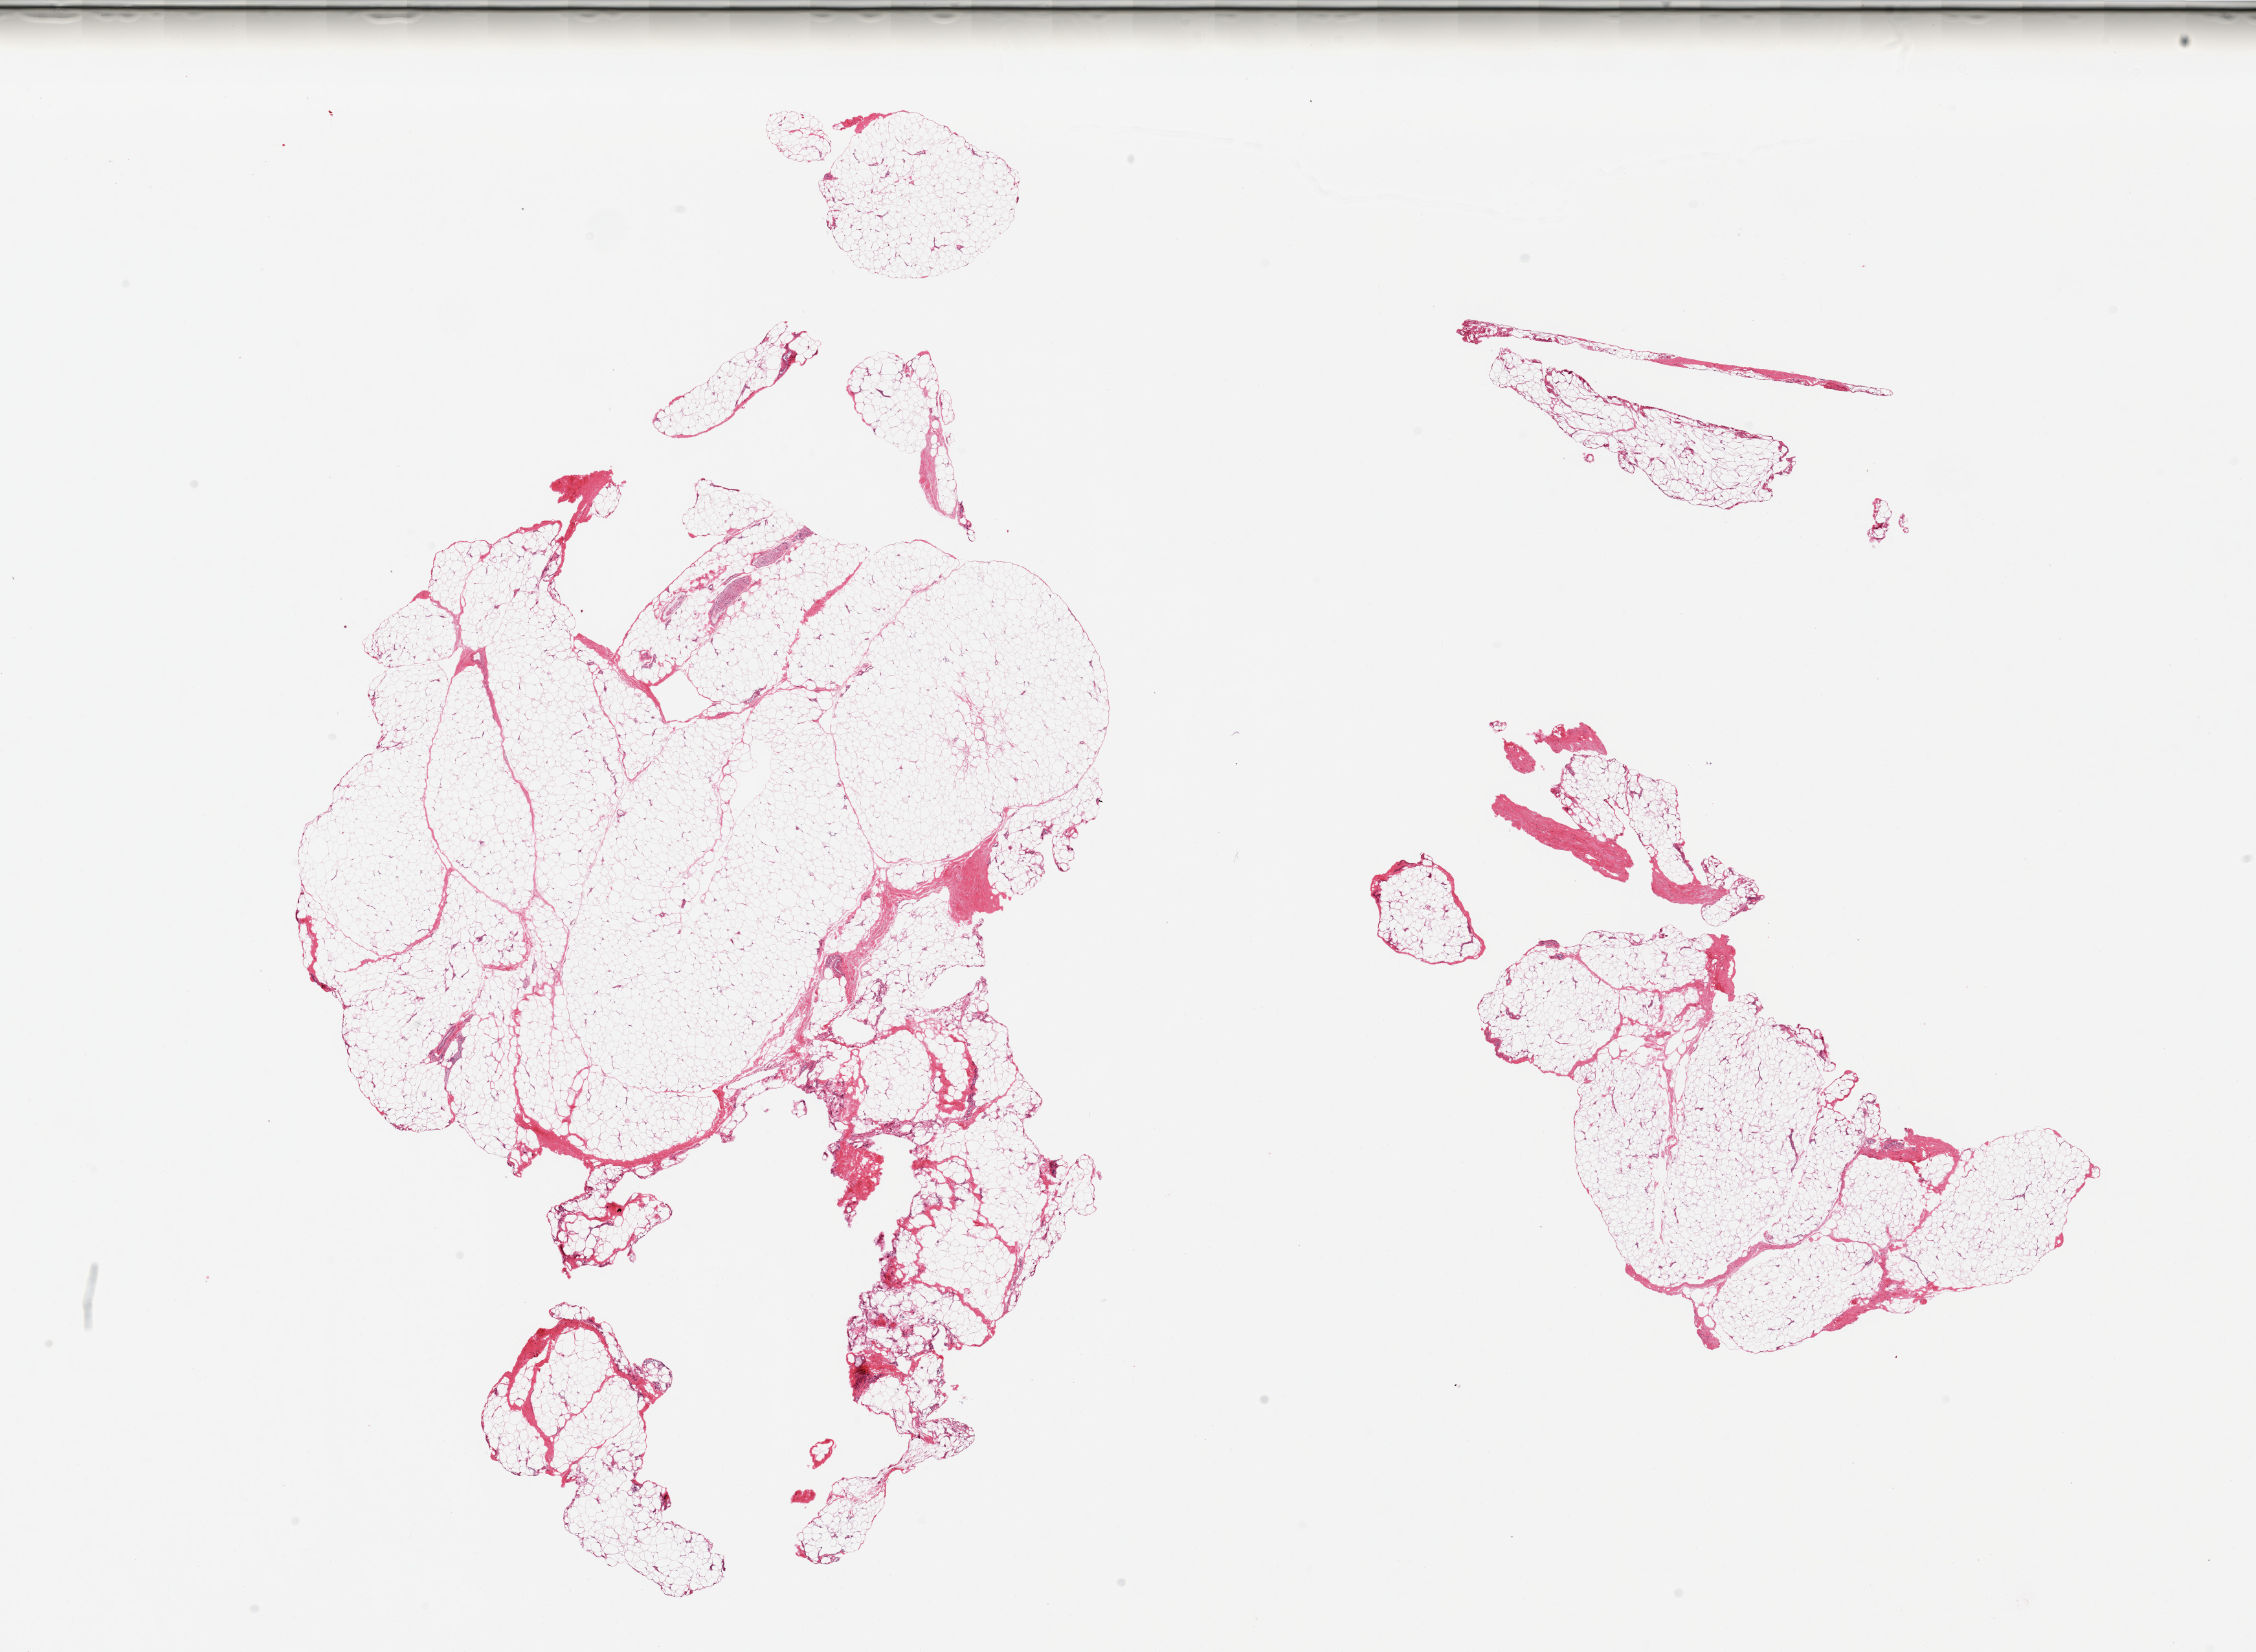
Digitized haematoxylin and eosin-stained section — shown as a low-resolution overview of the whole scanned area (about 27.6 x 20.2 mm). PAXgene-fixed, paraffin-embedded tissue. Target tissue: adipose tissue. Donor tissue sample.
- review note (as recorded): 2 pieces, 5-10% fascia